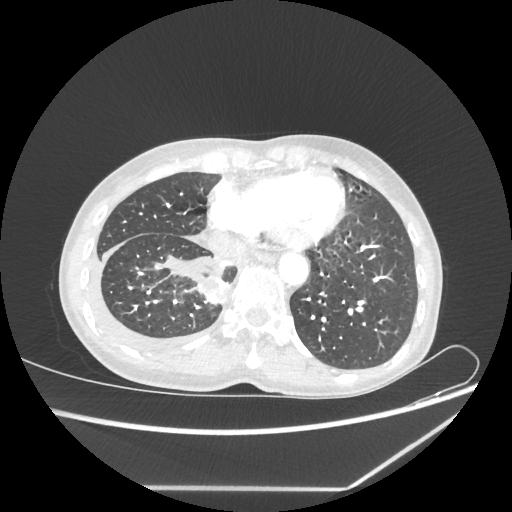
Chest CT, one axial slice; slice 63 of 237 in the series (ordered by position); 80 kVp; lung window (W 1500 / L -600 HU); 512 × 512 image matrix, field of view 364 × 364 mm. Female patient, age 59 years. Case-level facts recorded for this patient, not image findings: clinical TNM (as recorded): T1c N1 M1.
Outlined on this slice (bounding box drawn by a radiologist):
- lung tumour (recorded histology: adenocarcinoma): bounding box <199,277,229,304> (left, top, right, bottom; pixels)